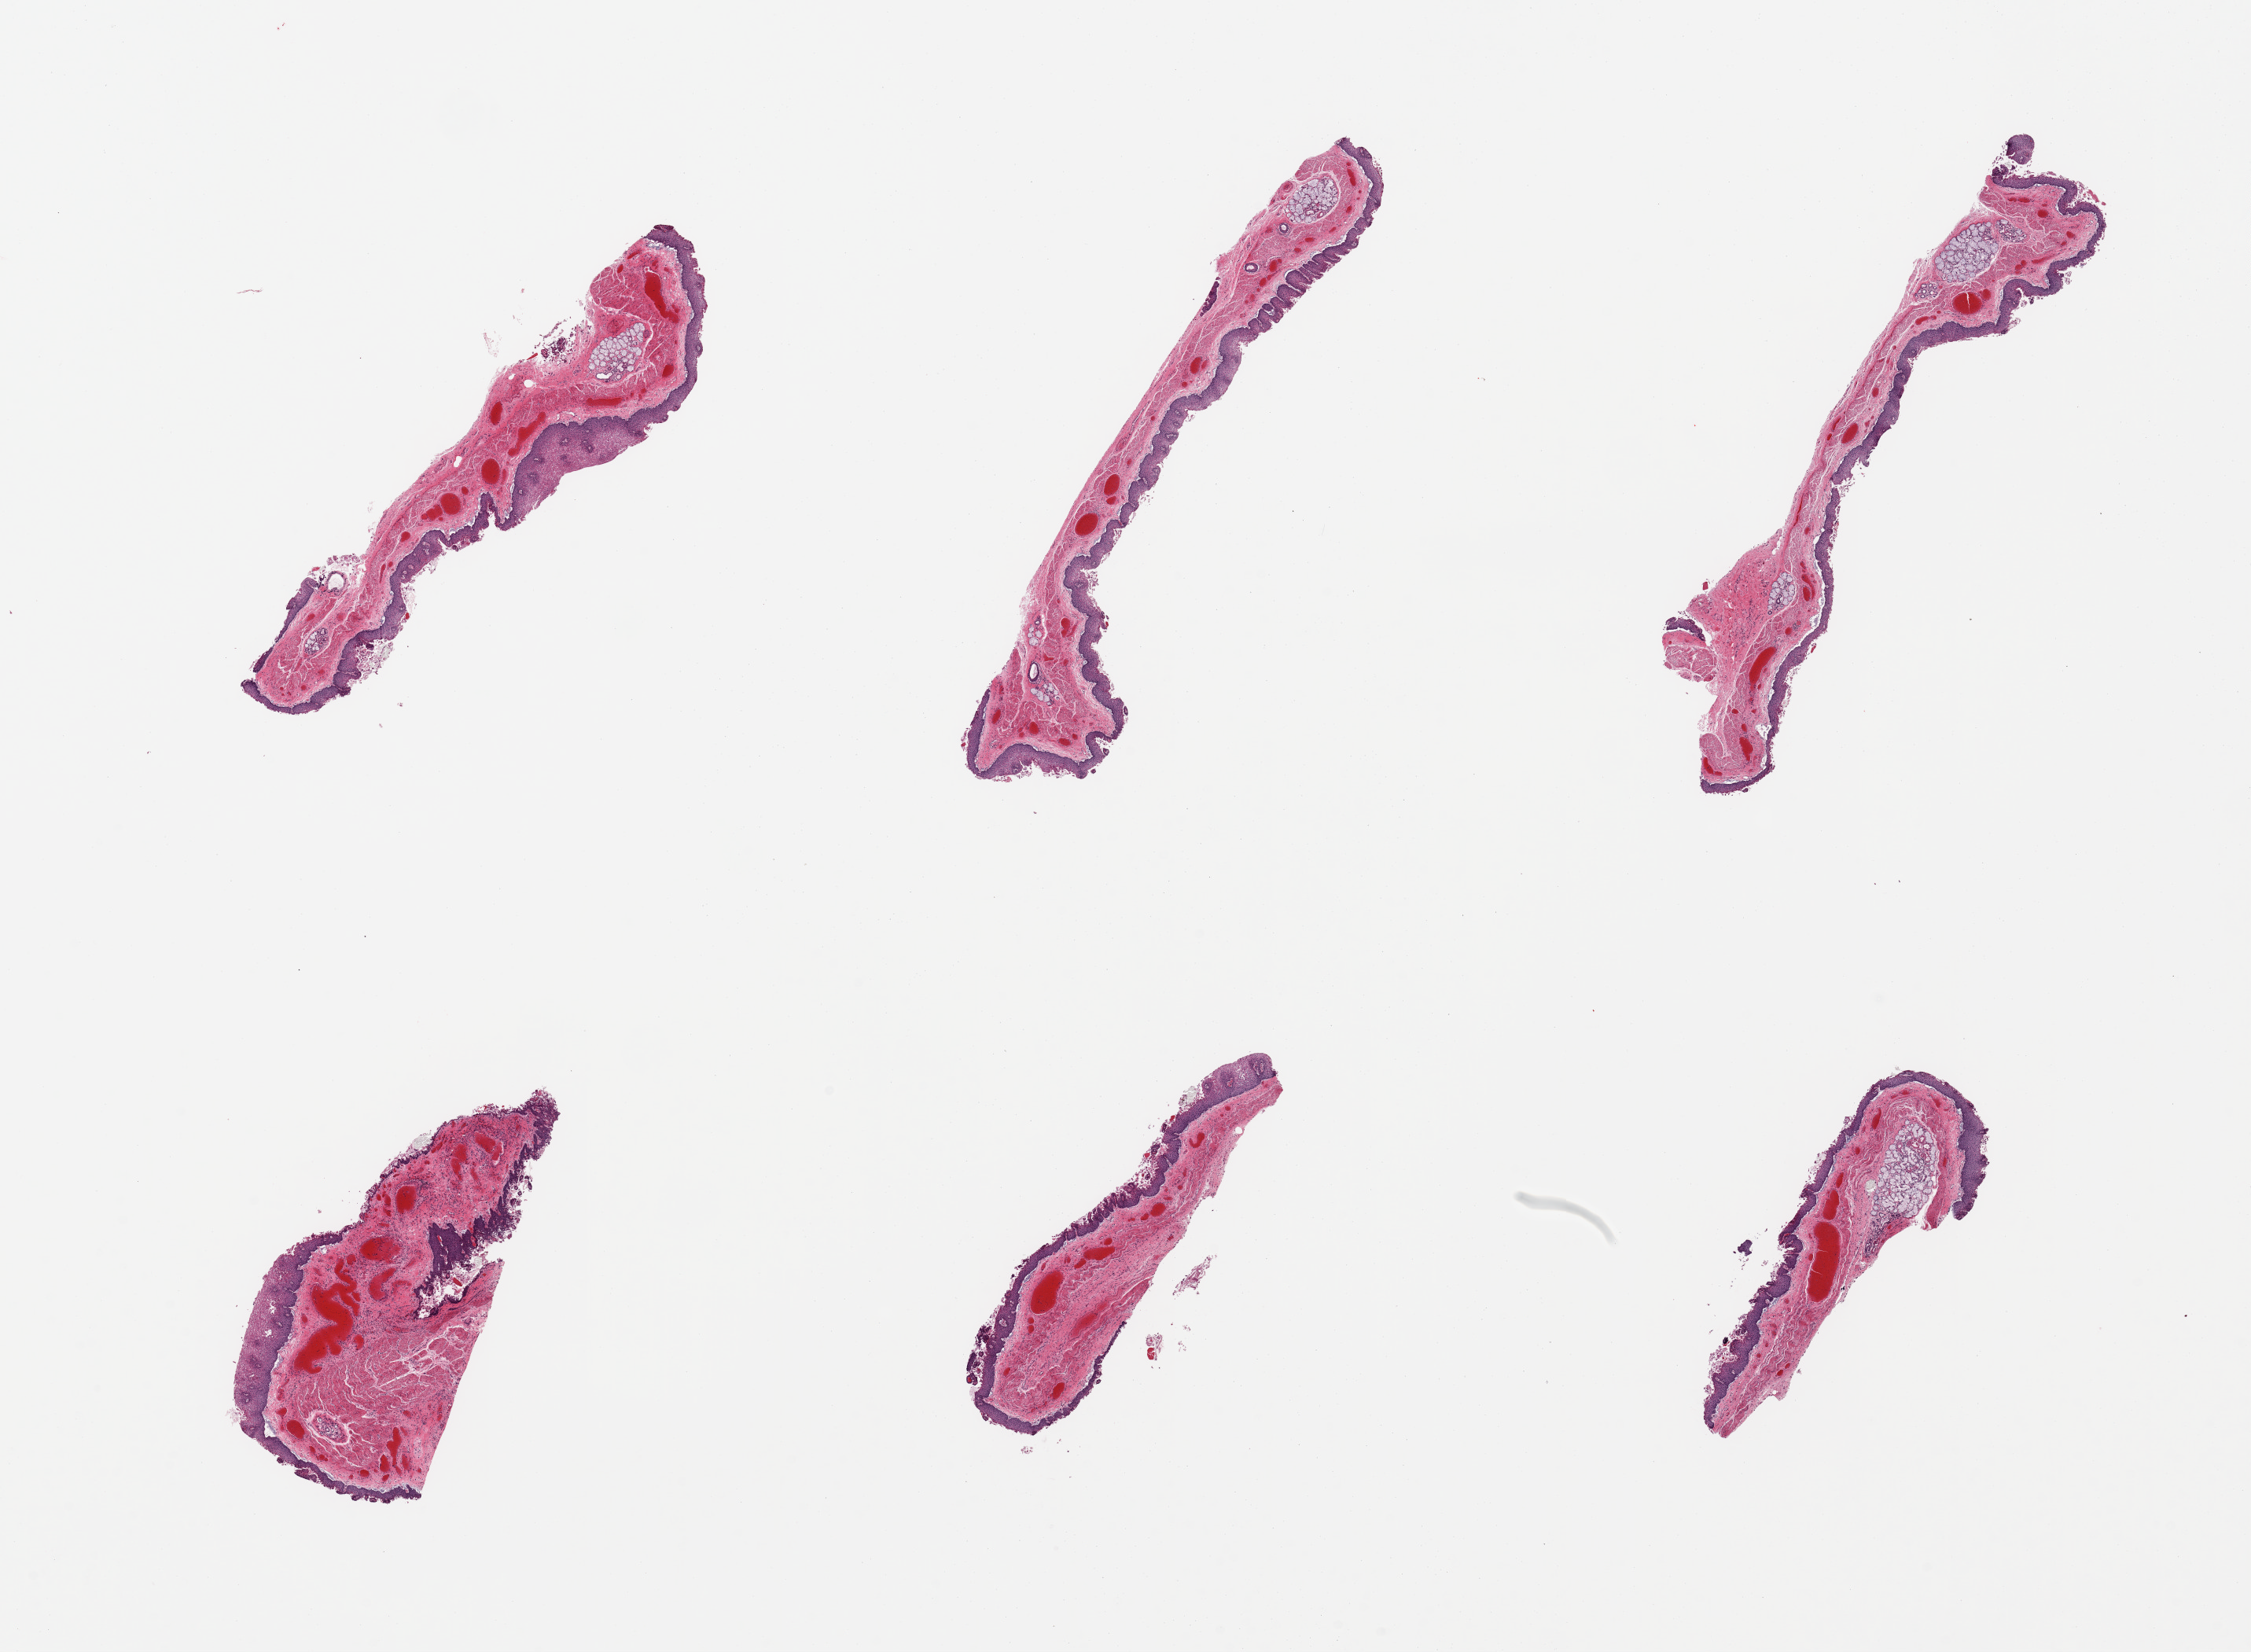
Hematoxylin and eosin (H&E) whole-slide image, a low-resolution overview of the entire scanned area, about 22.6 x 16.6 mm (slide scanned at 20x). PAXgene-fixed paraffin-embedded (PFPE) section. Sampled site (target tissue): esophageal mucous membrane. Donor tissue sample. Female donor.
Reviewer comment on this tissue sample: 6 pieces; moderate epithelium sloughing.